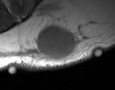
MRI of an extremity soft-tissue mass, one axial slice; slice 23 of 35 in the series (ordered by position); MR volume resampled by the dataset authors to the PET/CT grid (not the native acquisition matrix); 3.27 mm slice thickness; 115 × 90 image matrix, field of view 112 × 88 mm. Male patient. From the clinical record (not read from this slice): histological type: pleiomorphic leiomyosarcoma; grade: high; site of the primary tumour: left buttock.
Annotated regions visible in this slice (expert contour drawn on MRI and transferred to this co-registered scan by the dataset authors):
- gross tumour volume including surrounding oedema: box from (x=33, y=25) to (x=75, y=60) px
- gross tumour volume (mass): (x=35, y=25)–(x=75, y=60)